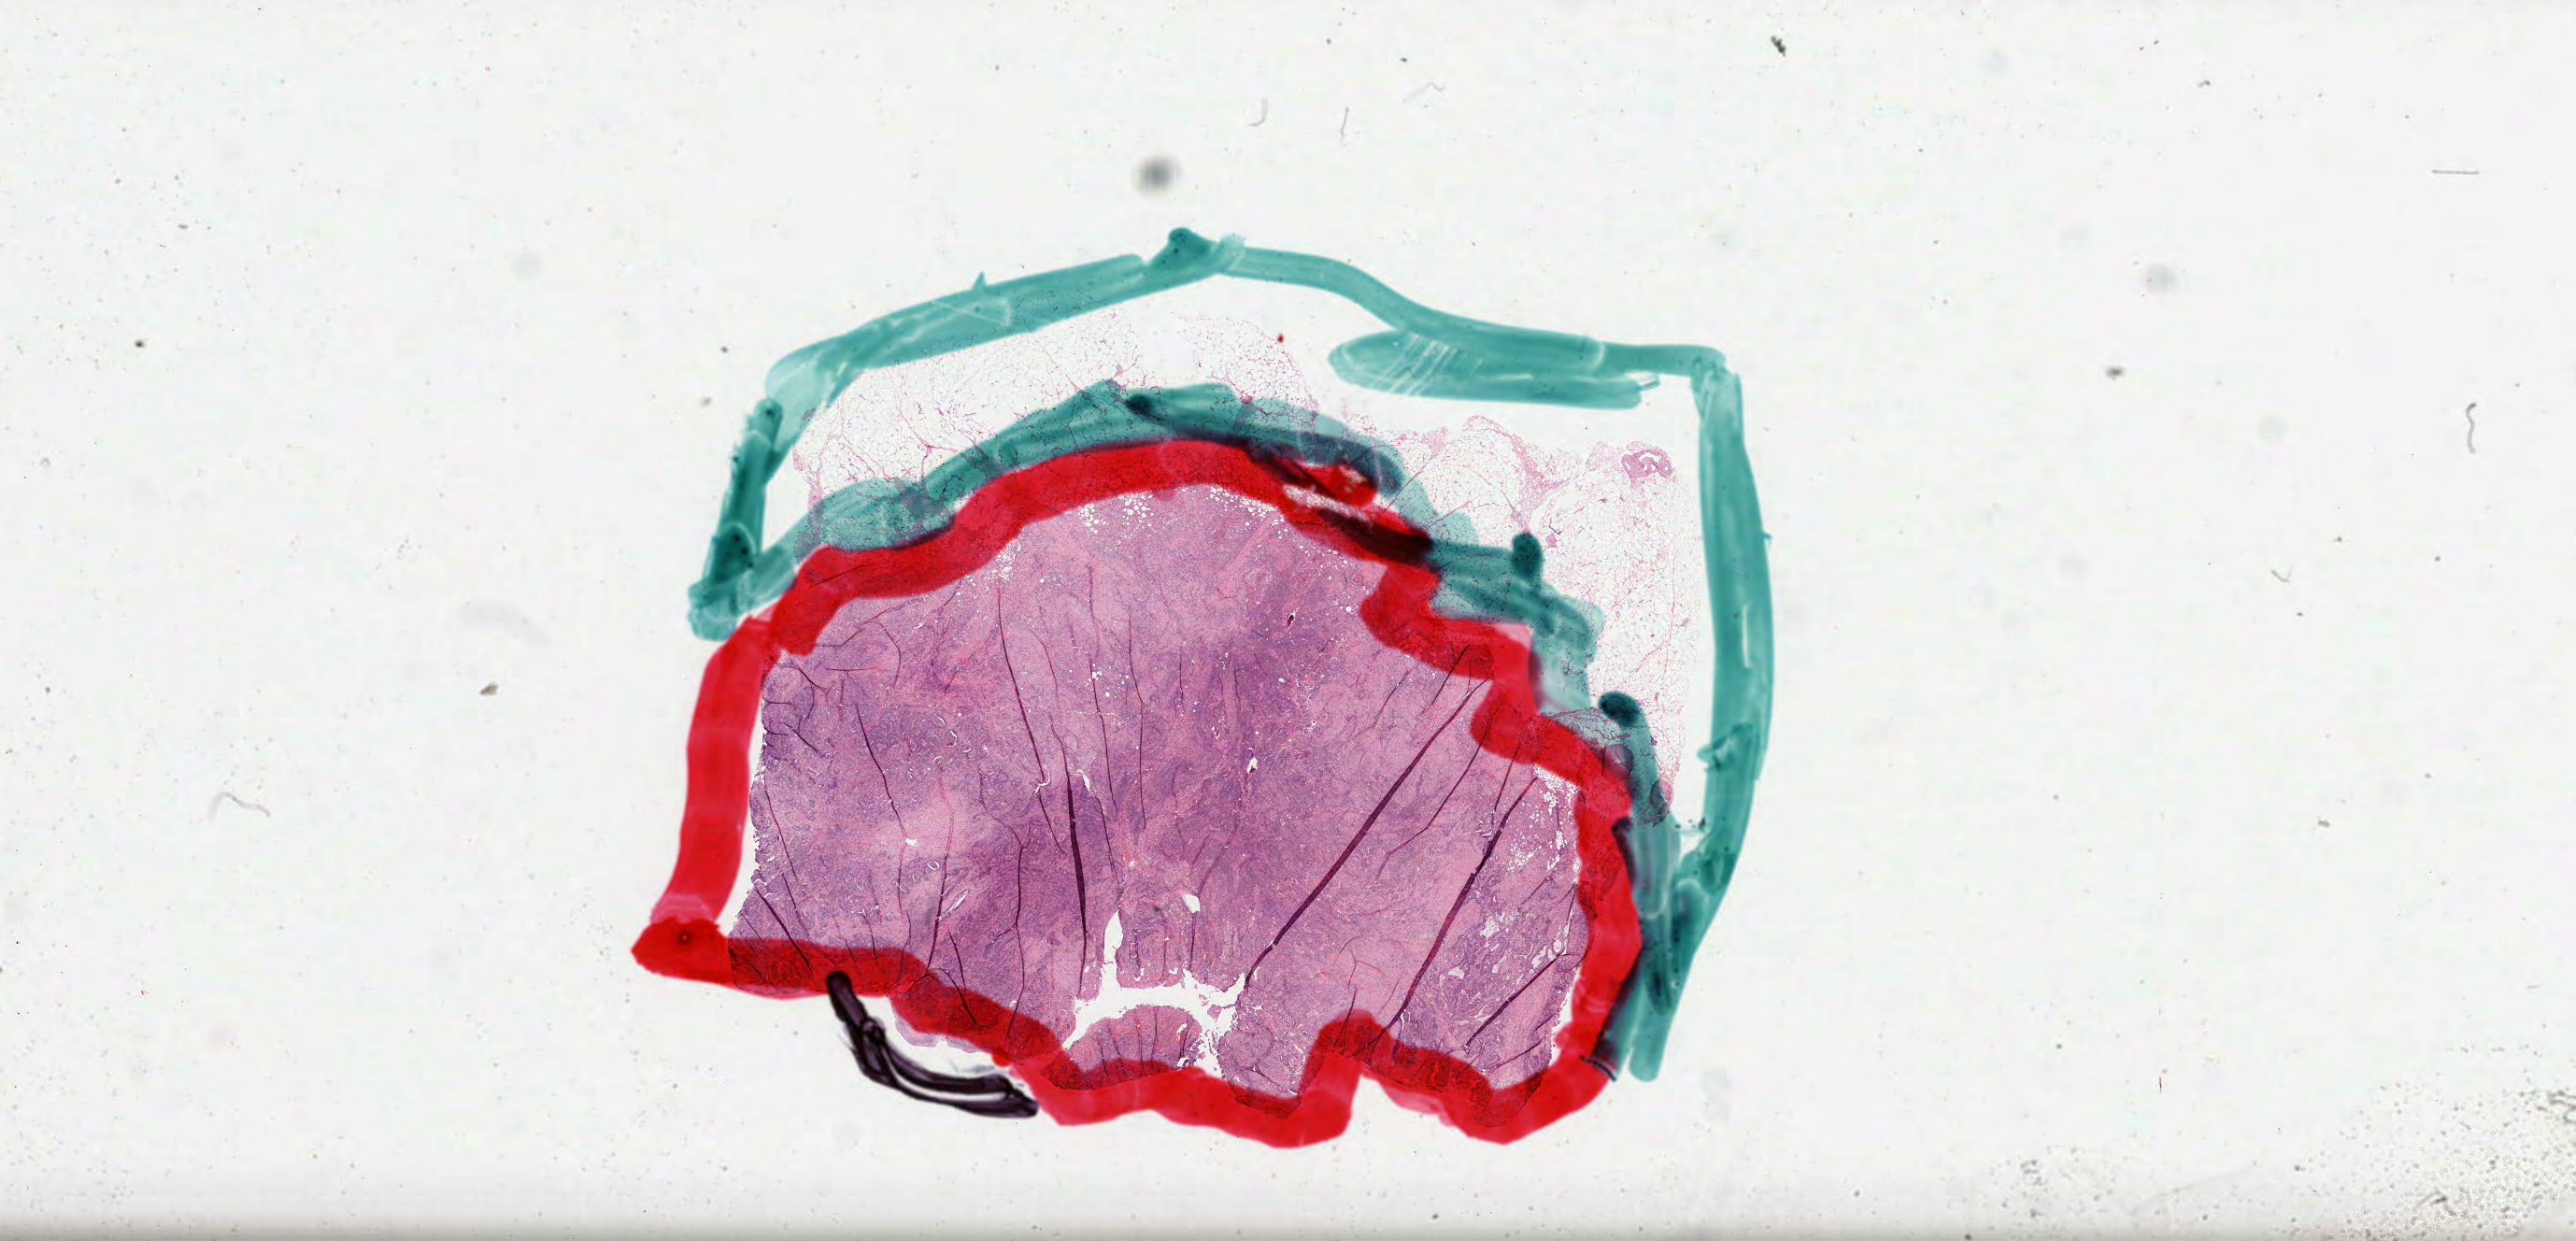
Hematoxylin and eosin (H&E) stained whole-slide image — whole scanned area (about 44.5 x 21.4 mm) shown as a low-resolution overview. Formalin-fixed paraffin-embedded (FFPE) diagnostic section. Primary tumour sample from the colon. Patient: male, age at initial diagnosis 64 years.
Diagnosis: Adenocarcinoma, NOS (ascending colon). Lymph nodes positive (case pathology): 0 of 12 examined. AJCC pathologic stage: IIA (7th edition).